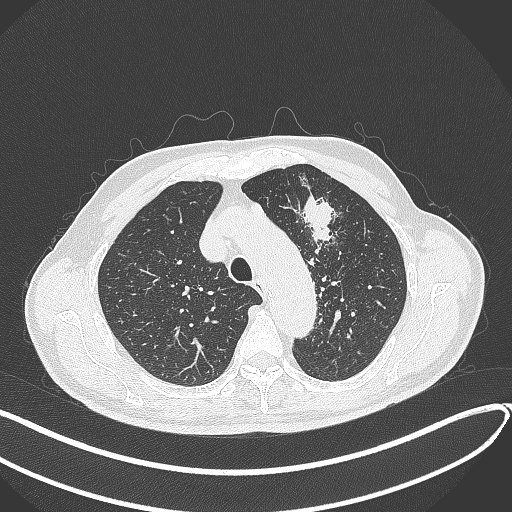
Chest CT, one axial slice. Position 318 of 459 along the scan axis. 120 kVp. Lung window (W 1500 / L -600 HU). 1 mm slice thickness. 512 × 512 image matrix. Patient: male, 74 years. From the clinical record (not read from this slice): clinical TNM (as recorded): T2b N0 M1c.
Structures marked on this image (rectangle marked by the reading radiologist):
- lung tumour (recorded histology: adenocarcinoma): bounding box [x1, y1, x2, y2] px = [300, 189, 342, 251]